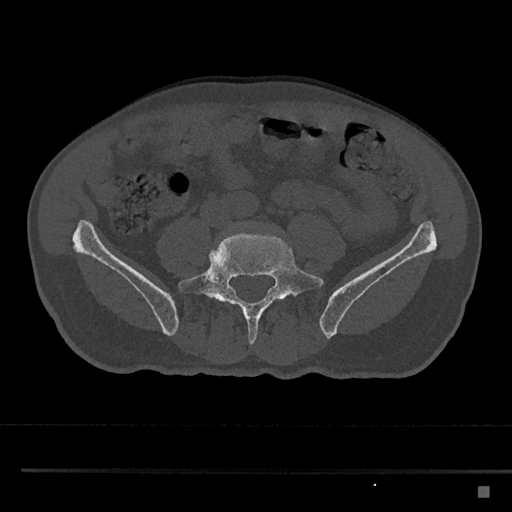
CT including the spine, one axial slice. Slice 588 of 797 in the series (ordered by position). Reconstruction kernel Br40s/3. 120 kVp. Bone window (W 1800 / L 400 HU). 0.5 mm slice thickness. 512 × 512 image matrix, field of view 391 × 391 mm. Male patient, age 59 years. From the clinical record (not read from this slice): primary cancer: prostate.
Annotated regions visible in this slice (semi-automatically segmented with operator editing):
- L5 vertebra: bounding box <178,231,324,345> (left, top, right, bottom; pixels)